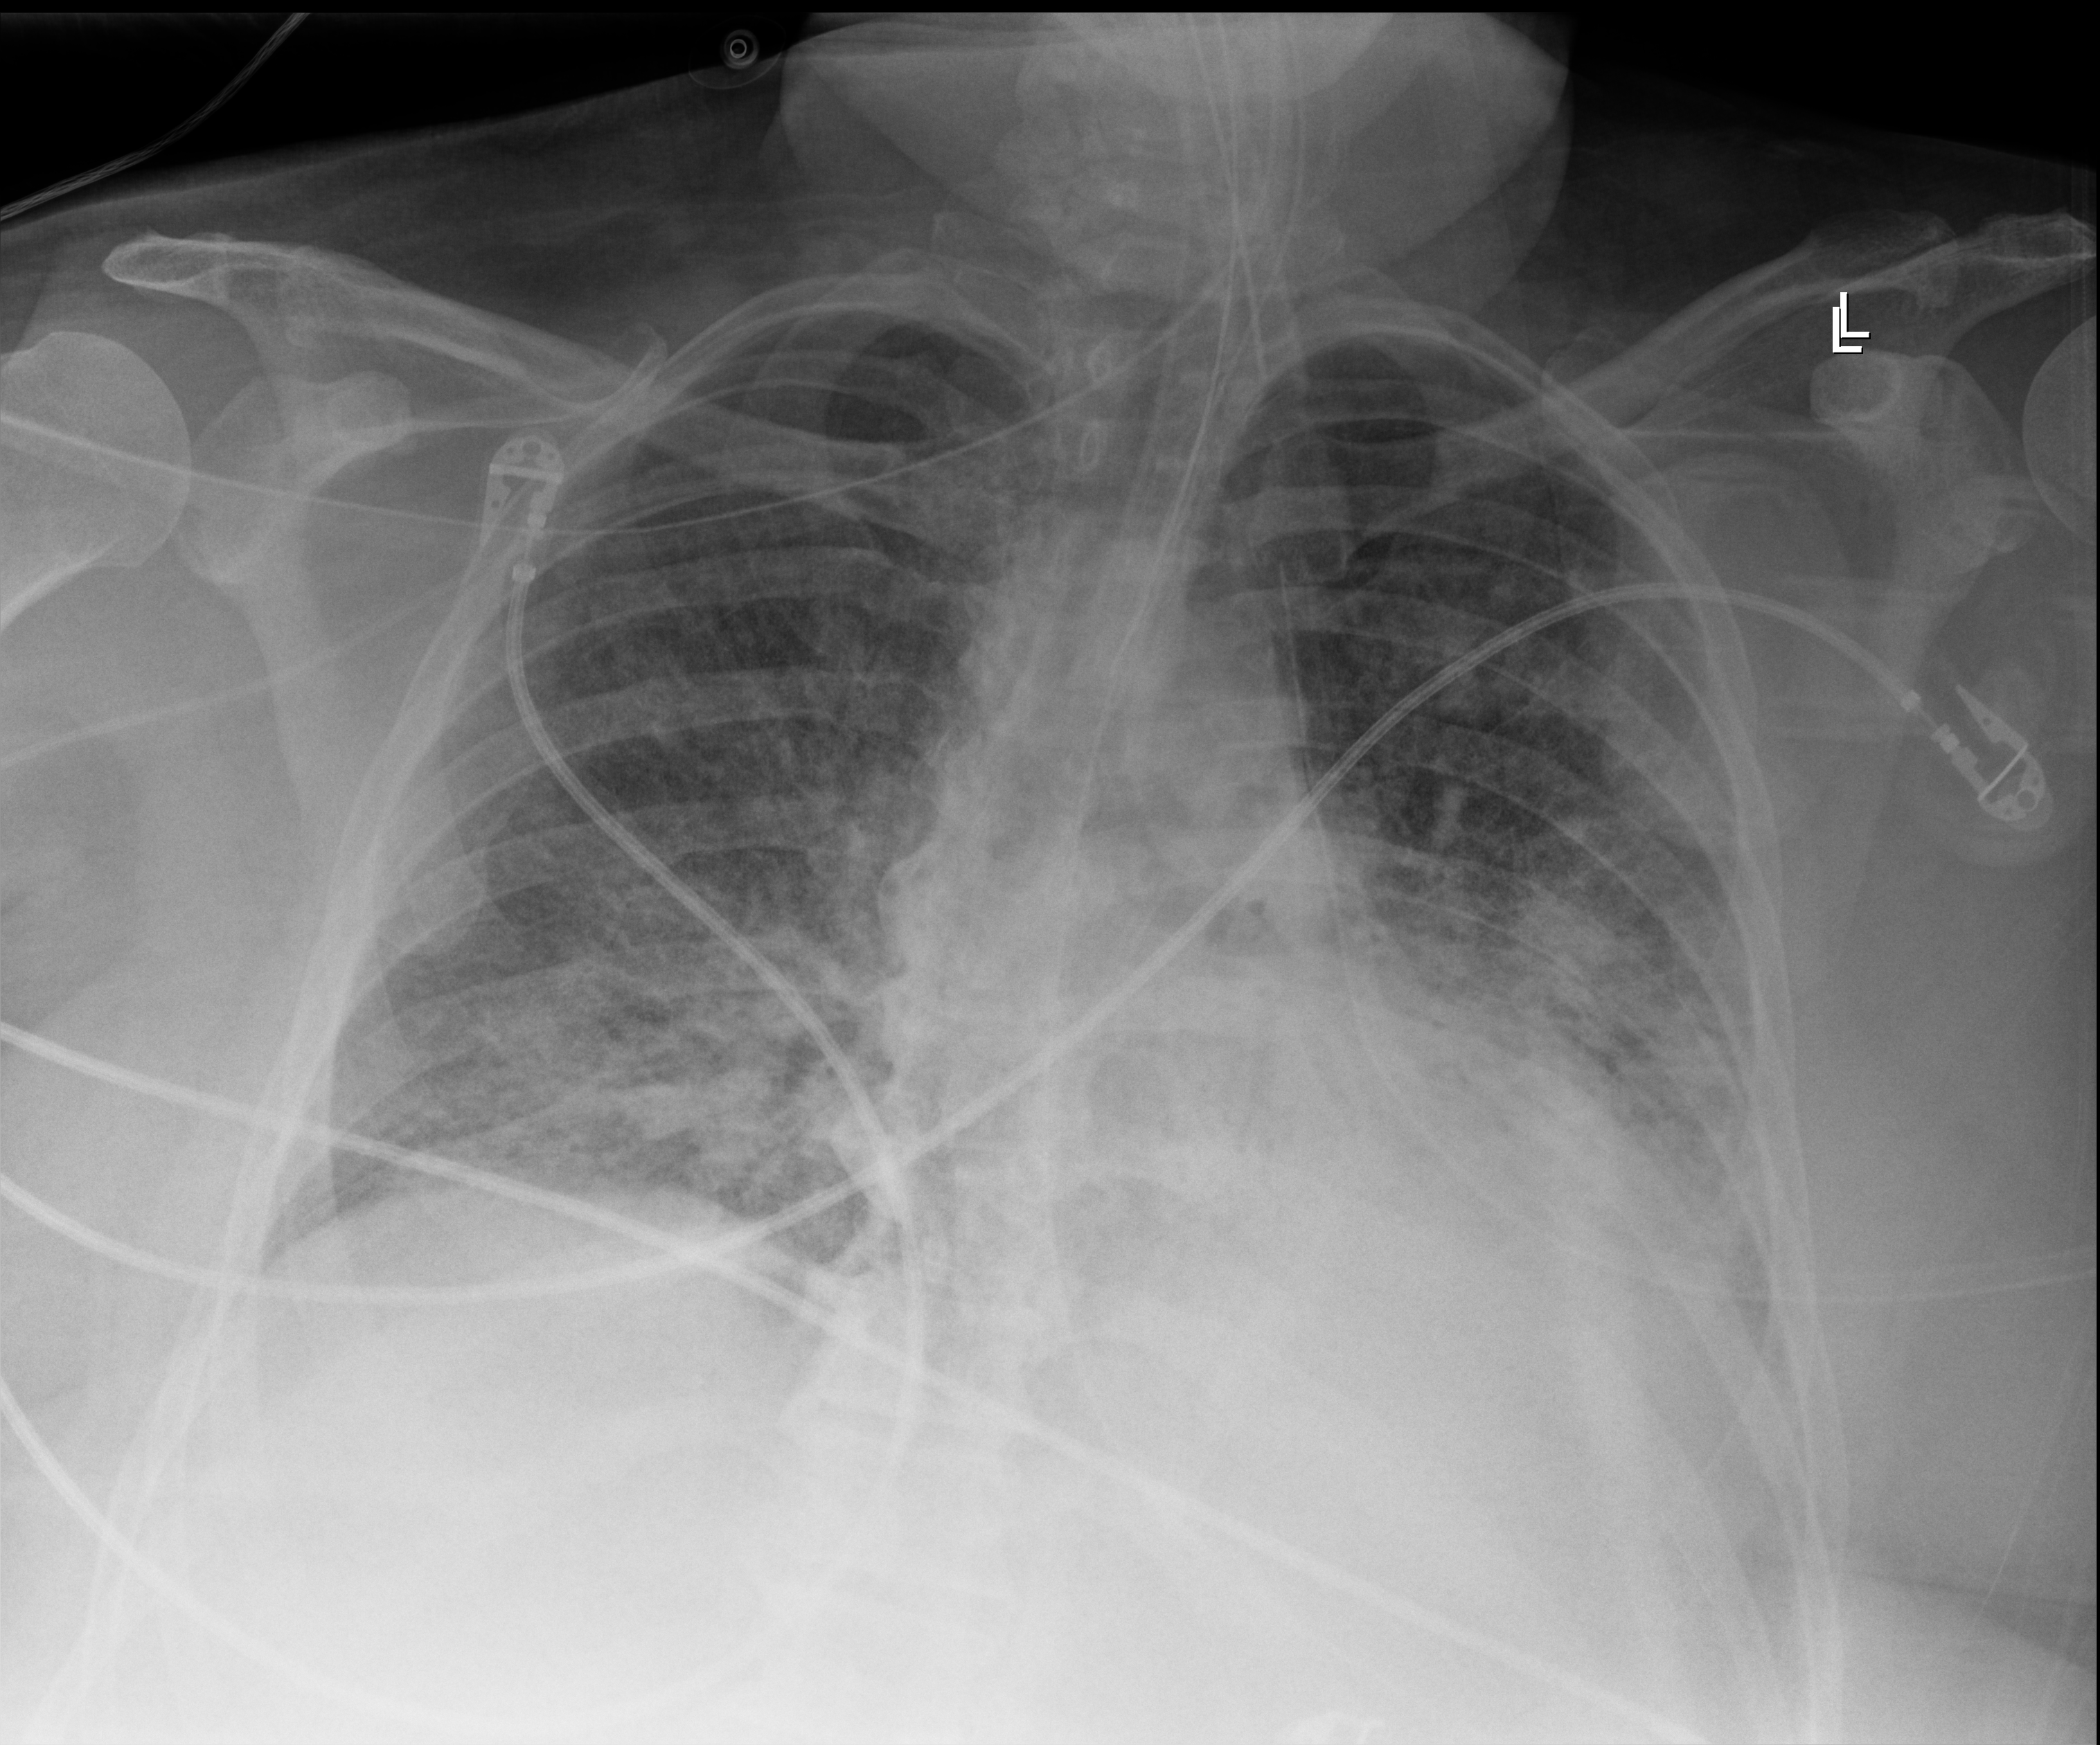
Chest X-ray. Adult patient hospitalised with COVID-19, age 18–59 years.
Admission-level facts for this patient (not findings on this image; timing relative to this image not recorded): admitted to intensive care during this hospital stay: yes.